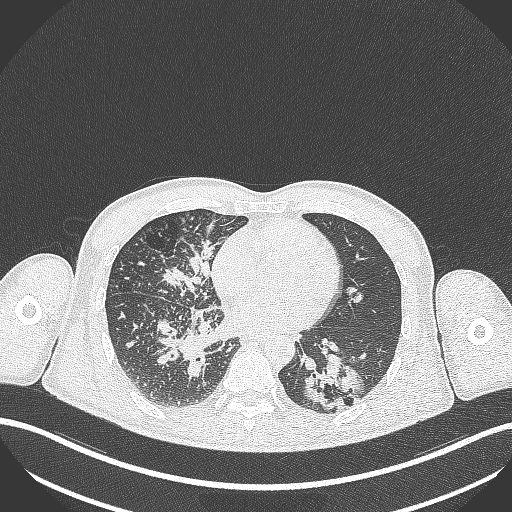
Chest CT, one axial slice. Position 129 of 348 along the scan axis. Reconstruction kernel B70f. 120 kVp. Lung window (W 1500 / L -600 HU). 1 mm slice thickness. 512 × 512 image matrix, field of view 400 × 400 mm. Male patient, age 49 years. Case-level facts recorded for this patient, not image findings: clinical TNM (as recorded): T2b N1 M0.
Annotated regions visible in this slice (bounding box drawn by a radiologist):
- lung tumour (recorded histology: adenocarcinoma): bounding box [x1, y1, x2, y2] px = [300, 350, 368, 411]